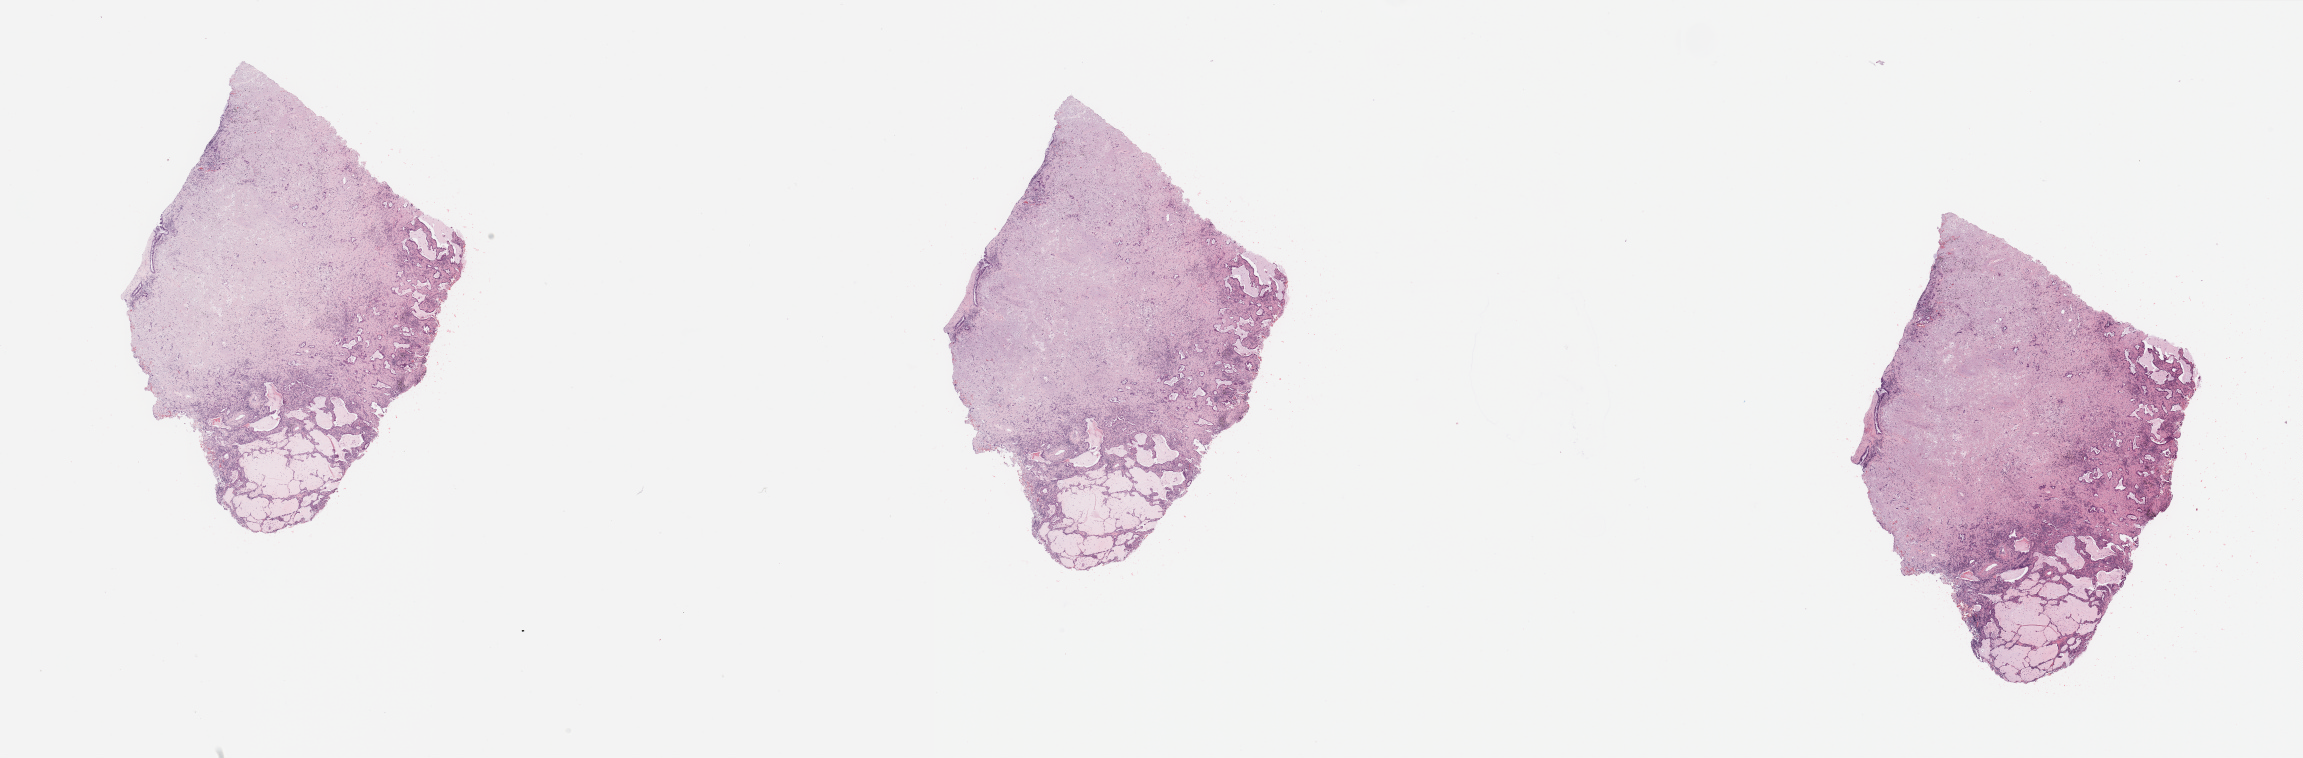
Whole-slide histology image, H&E-stained, low-resolution overview of the scanned area, about 36.4 x 12.0 mm (acquisition: 20x scan), lung, tissue type not recorded.
Patient diagnosis (cohort enrolment): lung adenocarcinoma (lung).